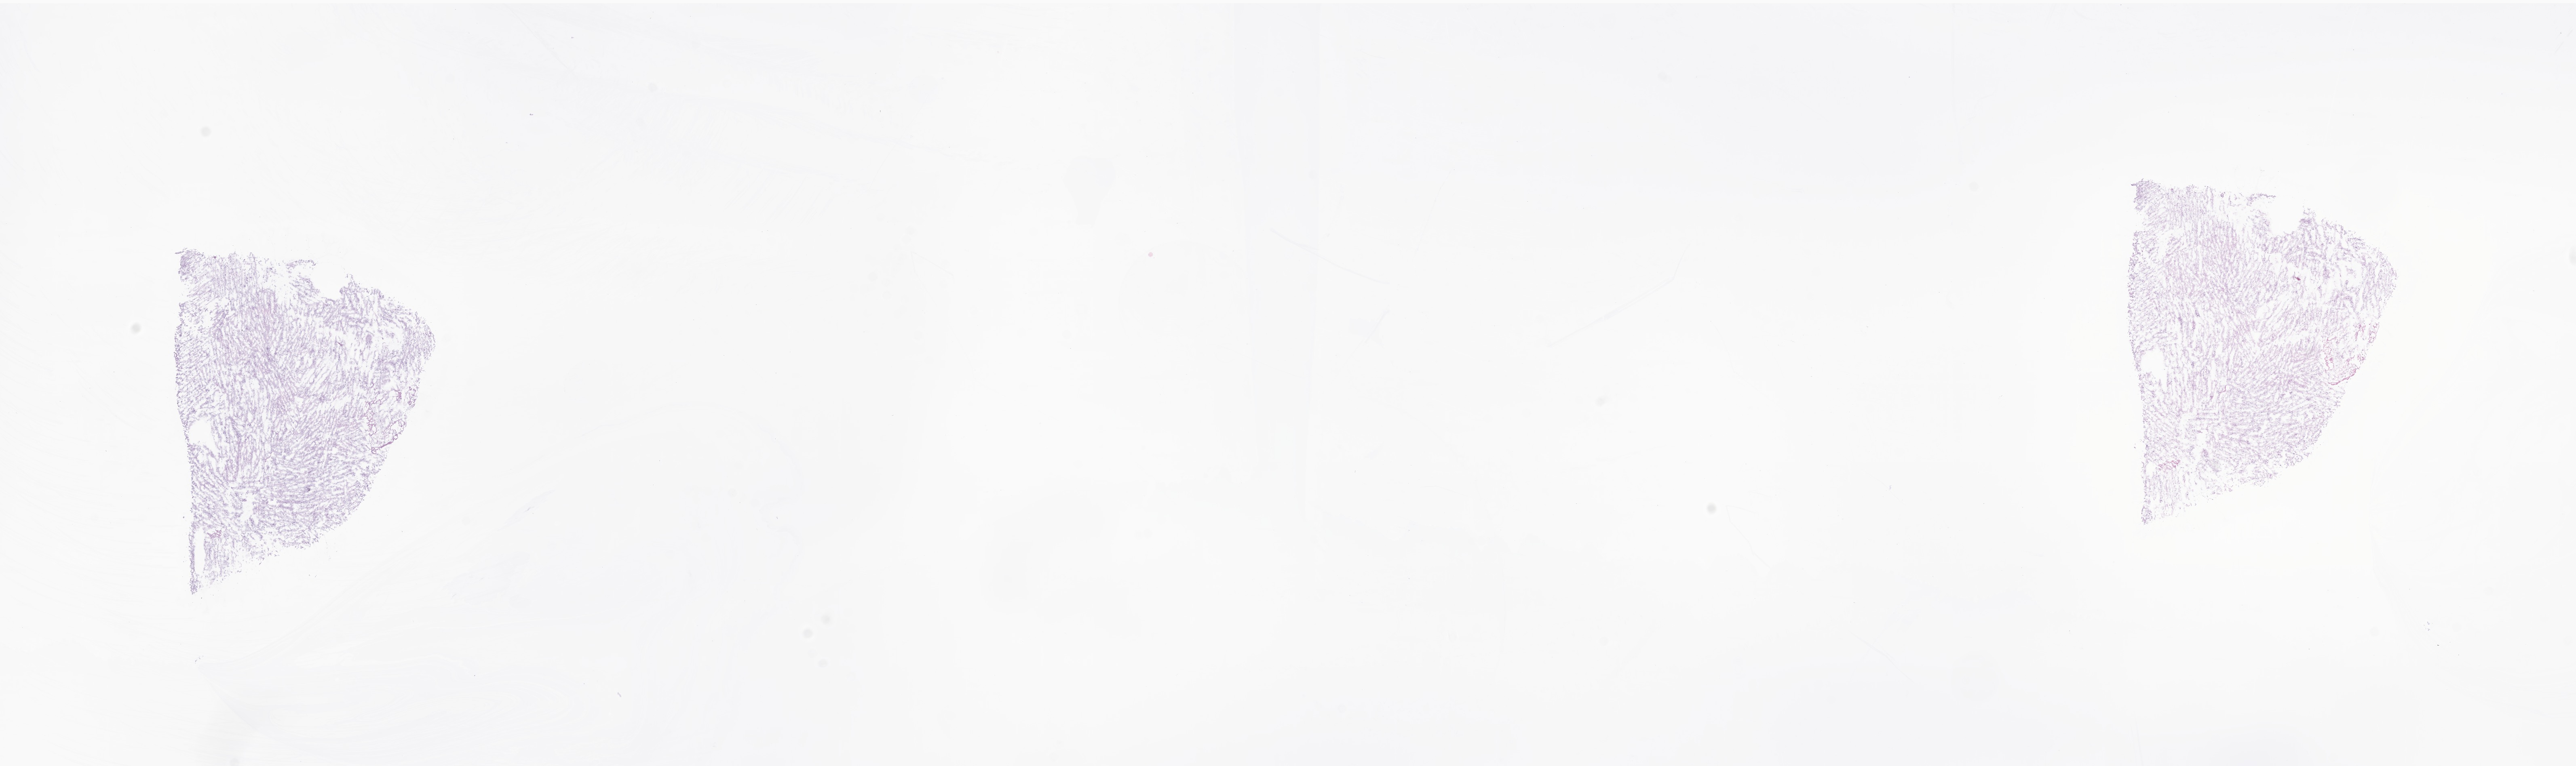
Digitized hematoxylin and eosin (H&E)-stained section of tumor tissue from the brain stem — a low-resolution overview of the entire scanned area, about 26.9 x 8.0 mm; frozen section (OCT-embedded). Patient: male, age 91 months (7 years 7 months).
Diagnosis: Glioma, malignant.